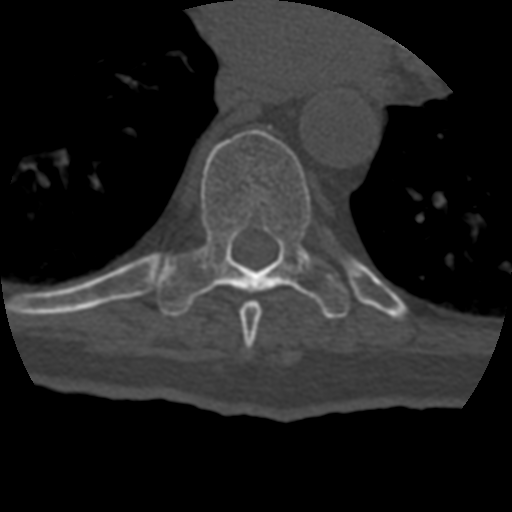
CT including the spine, one axial slice; position 244 of 399 along the scan axis; reconstruction kernel STANDARD; bone window (W 1800 / L 400 HU); 1.25 mm slice thickness; 512 × 512 image matrix, field of view 160 × 160 mm. Patient age 69 years. From the clinical record (not read from this slice): primary cancer: prostate.
Structures marked on this image (semi-automatically segmented with operator editing):
- T8 vertebra: bounding box (x1, y1, x2, y2) in pixels: (240, 300, 262, 348)
- T9 vertebra: (154, 129, 351, 319)